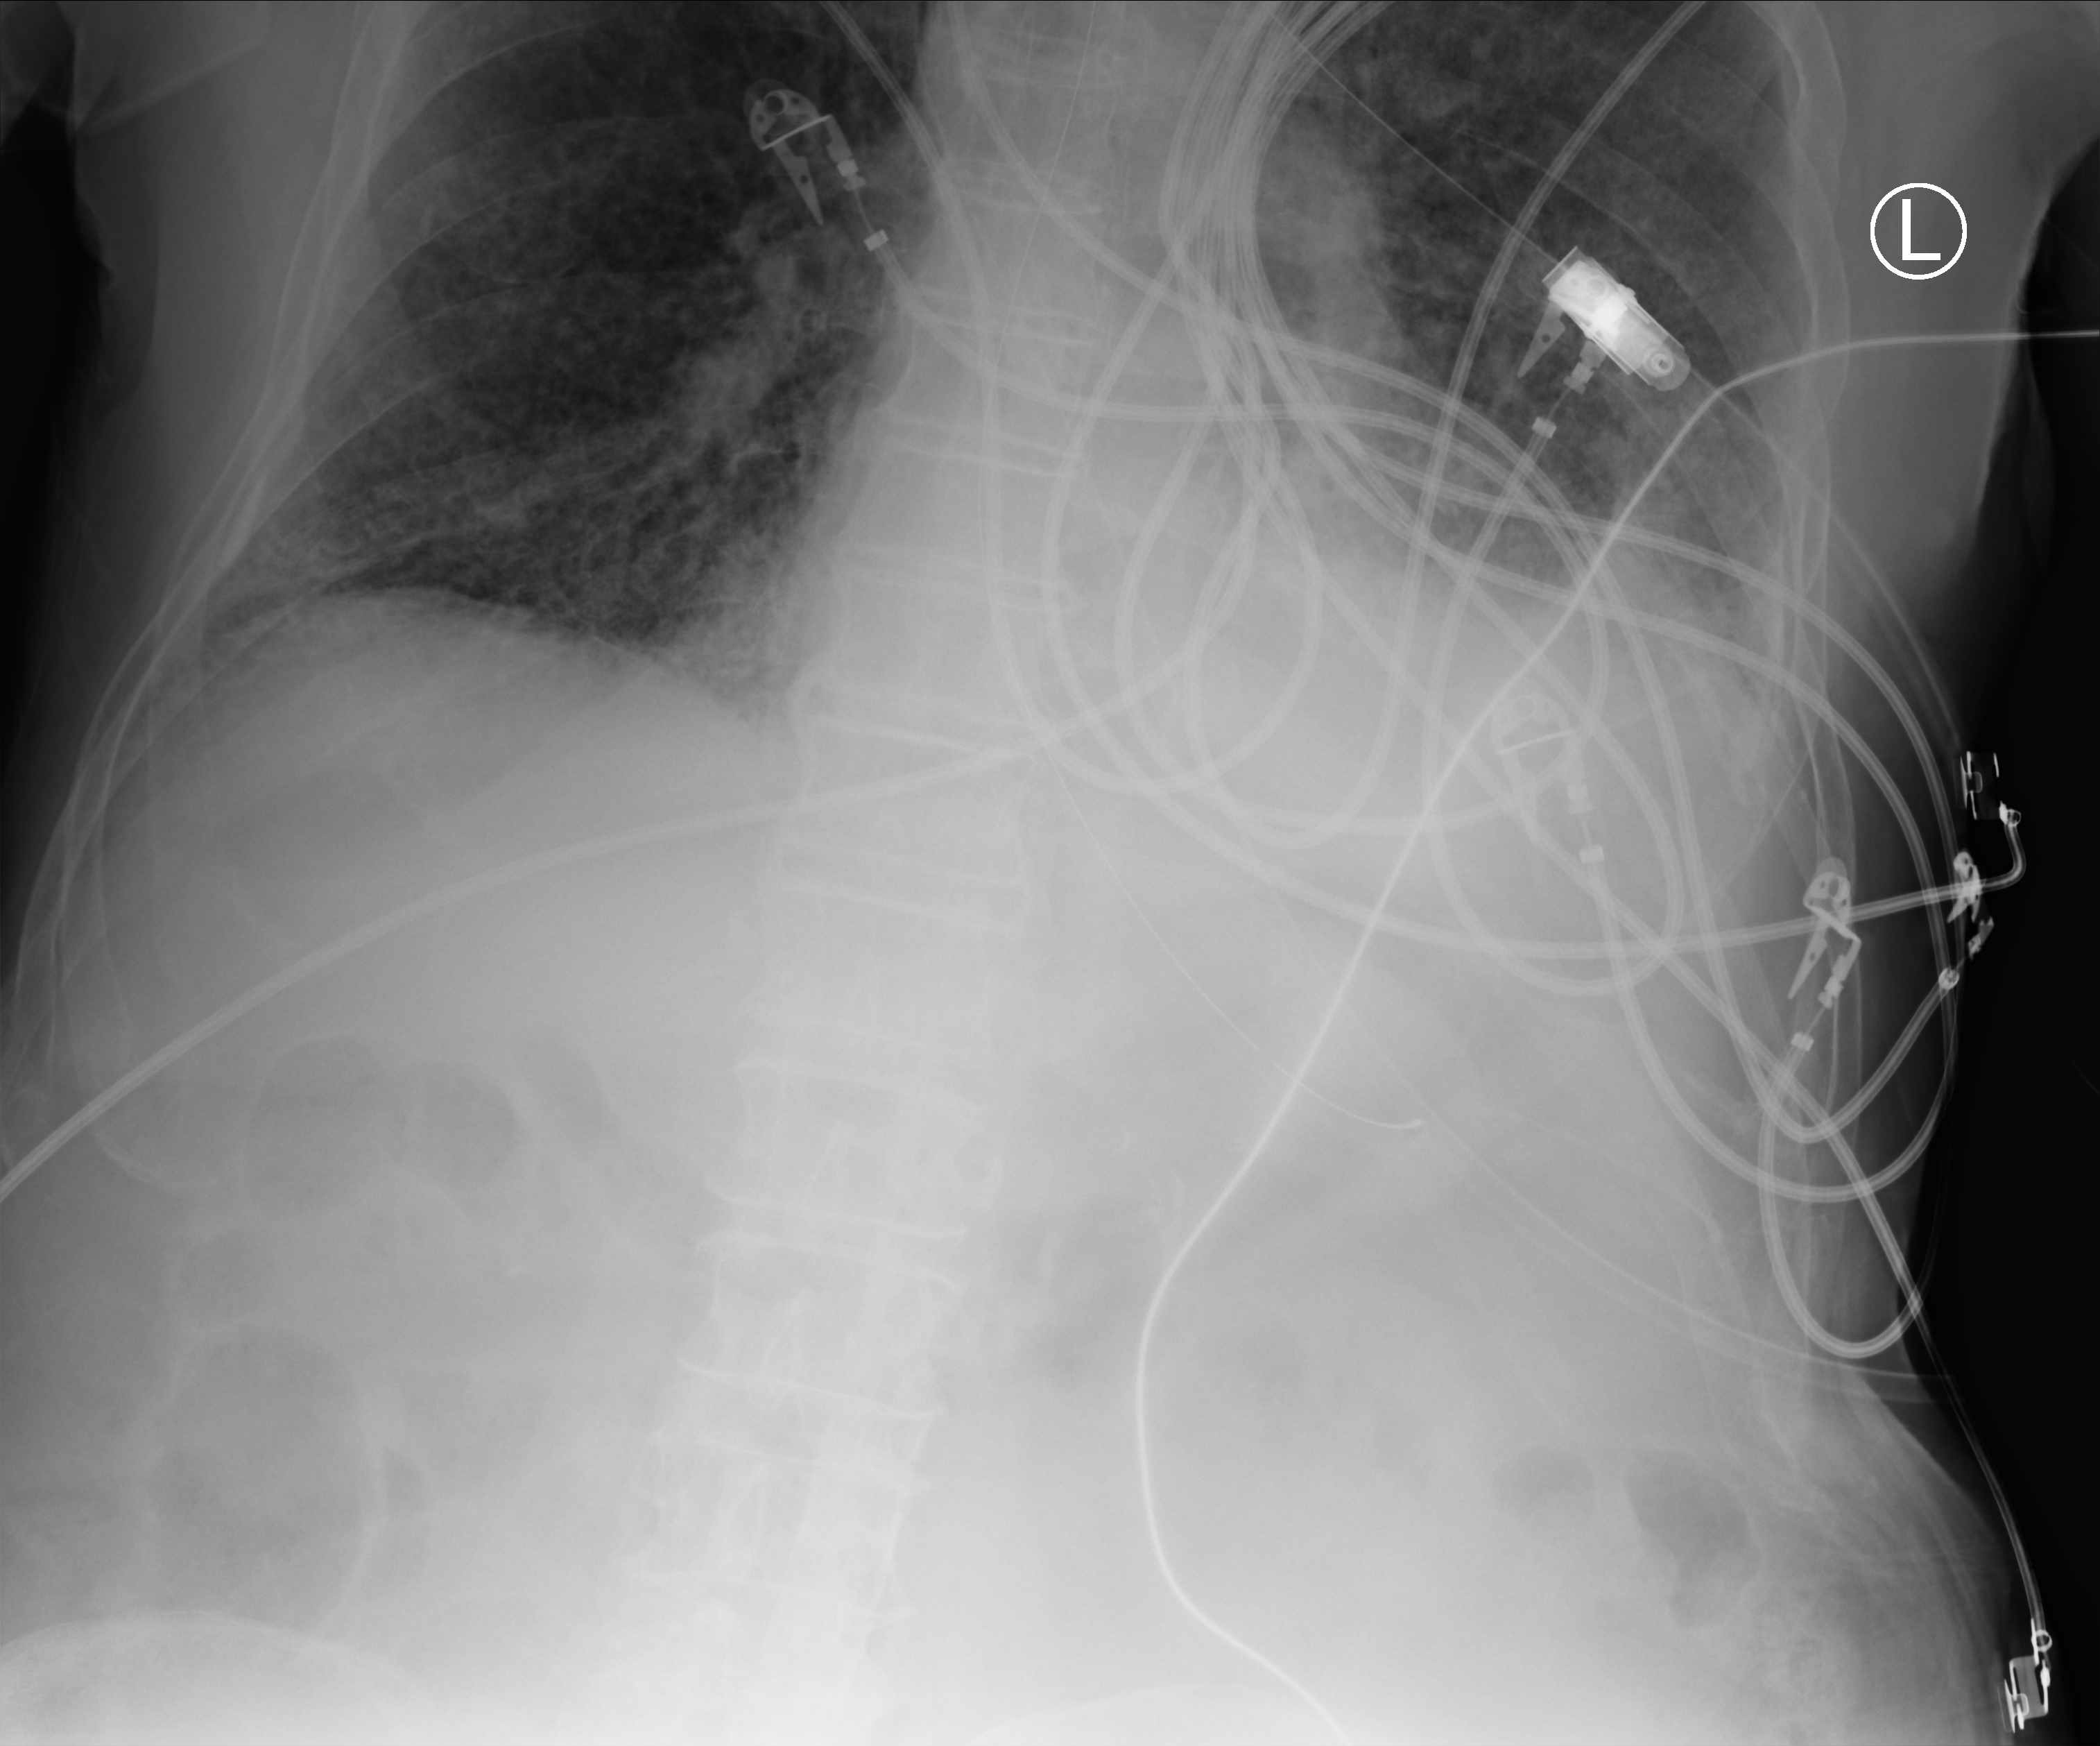
Portable chest radiograph. Patient hospitalised with COVID-19; male, aged 75–90 years.
Hospital-stay facts (about this admission, not read from this image; timing relative to this image not recorded): mechanically ventilated during this hospital stay: yes; length of hospital stay: 6 days; admitted to intensive care during this hospital stay: yes.